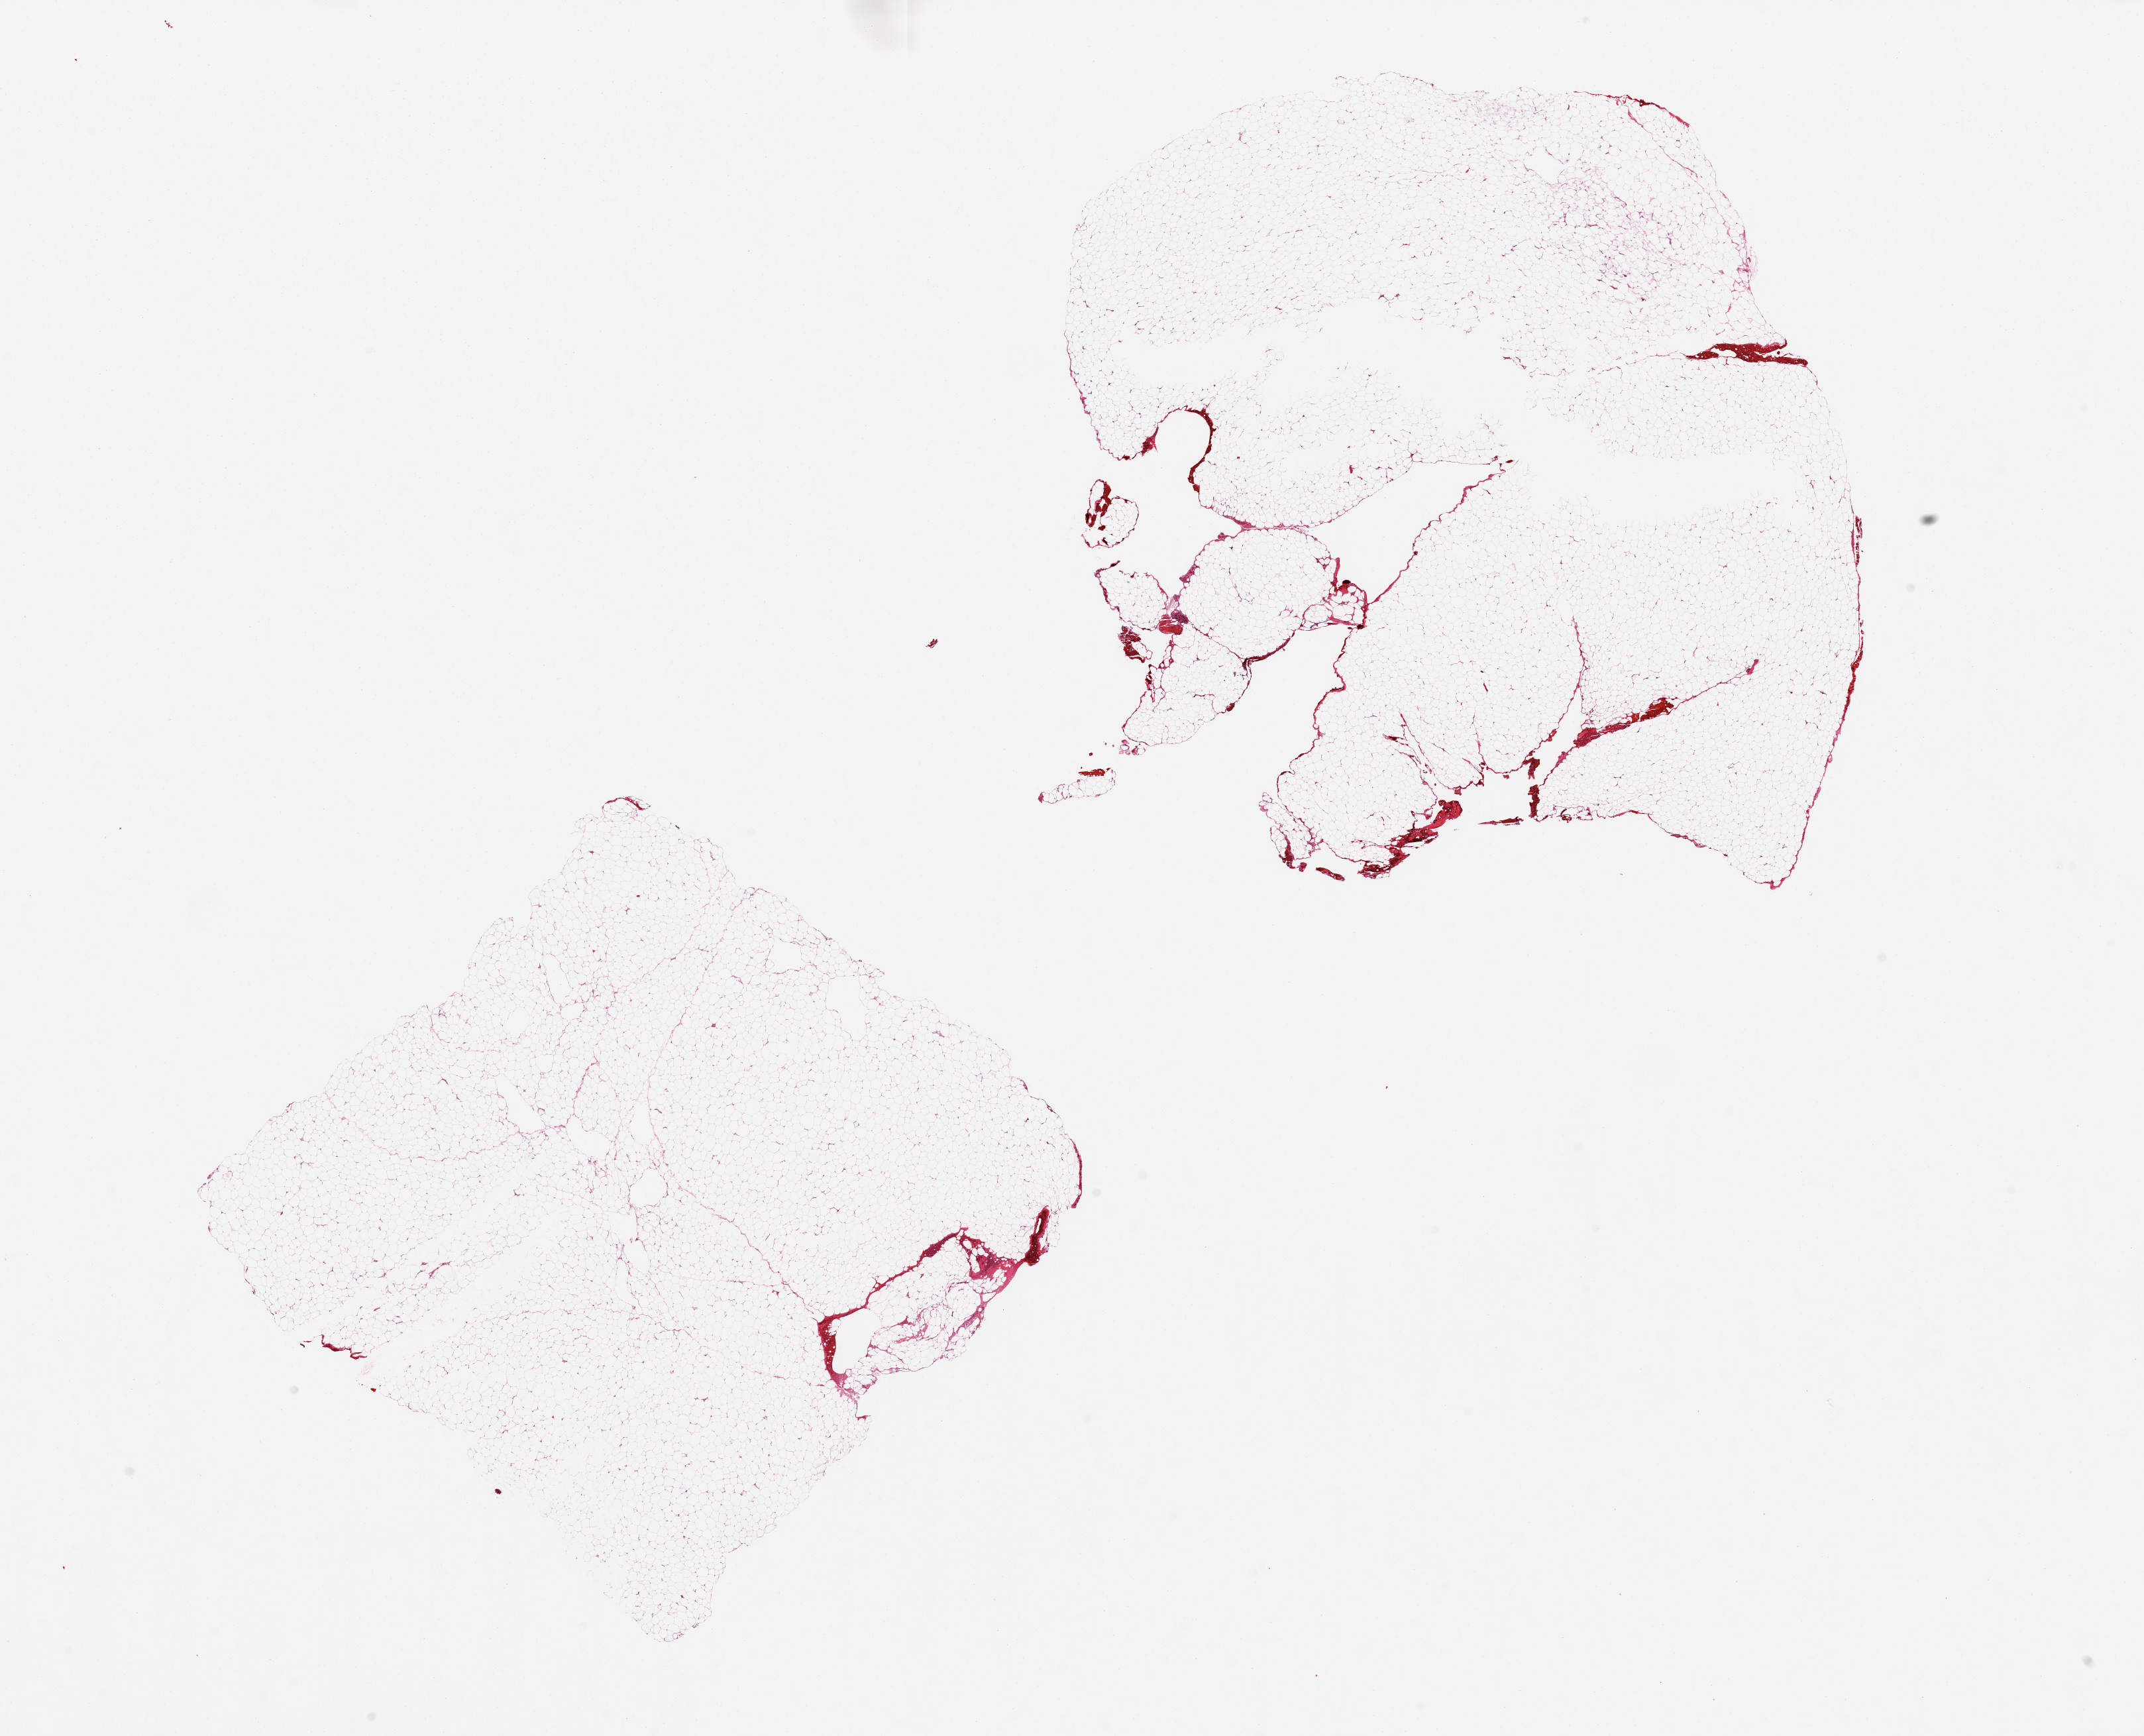
Whole-slide image, H&E stain — whole scanned area (about 25.6 x 20.7 mm) shown as a low-resolution overview; PAXgene-fixed paraffin-embedded (PFPE) section; sampled site (target tissue): omentum; donor tissue sample.
- reviewer comment on this tissue sample: 2 pieces, central defects in one piece